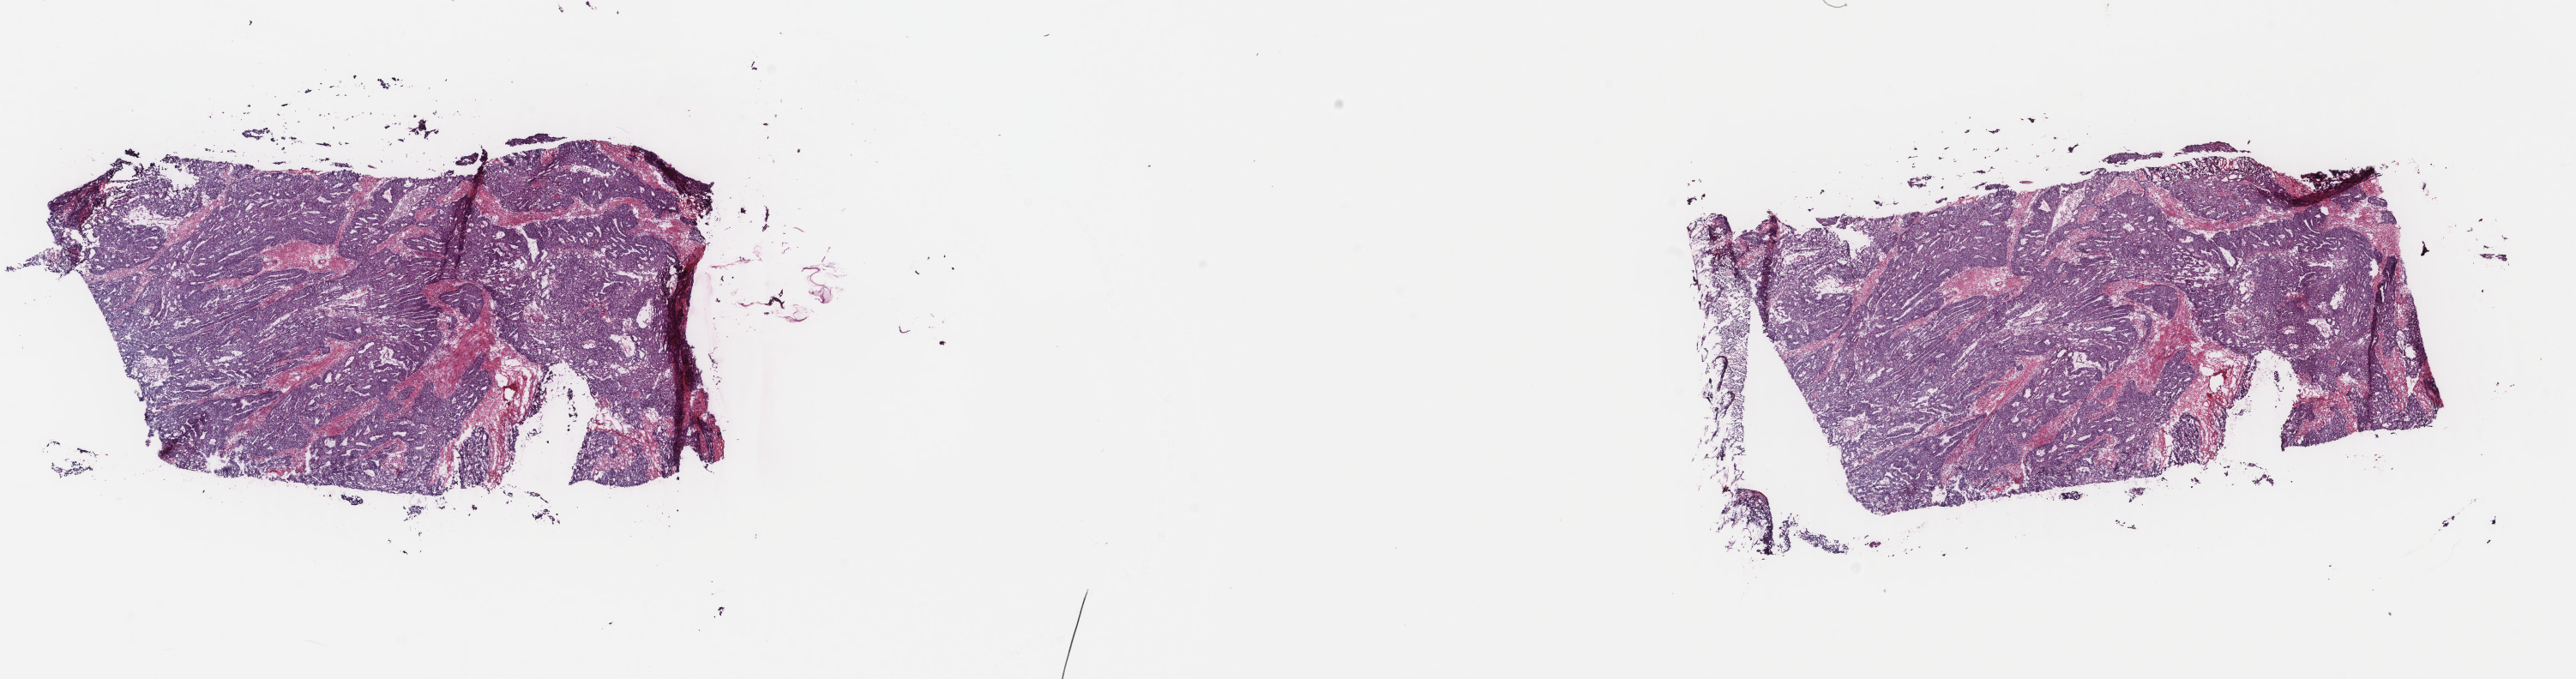
Hematoxylin and eosin (H&E) stained whole-slide image, whole scanned area (about 23.8 x 6.3 mm, slide scanned at 40x) shown as a low-resolution overview; frozen section from the top of the tissue portion; primary tumour sample from the uterus. Patient: female, age at initial diagnosis 41 years. Histologic grade: G3 (poorly differentiated). Slide review estimates, as recorded: tumour cells 75%, tumour nuclei 85%, normal cells 0%, stromal cells 25%, necrosis 0%. Infiltration values recorded for this section: lymphocyte infiltration 1%, monocyte infiltration 0%, neutrophil infiltration 0%.
FIGO stage: II. Pathologic diagnosis: Endometrioid adenocarcinoma, NOS (endometrium). Lymph nodes positive (case pathology): 0 of 11 examined.